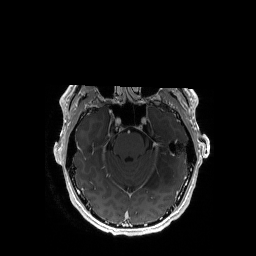
Brain MRI from a brain-tumour surgery series, one axial slice; position 120 of 192 along the scan axis; T1-weighted post-contrast; 1 mm slice thickness; 256 × 256 image matrix, field of view 256 × 256 mm. From the clinical record (not read from this slice): histopathology: Astrocytoma; WHO grade: 3; IDH mutation: yes; tumour location: Left Temporal.
Outlined on this slice (outlined manually by an expert reader):
- tumour: bounding box (x1, y1, x2, y2) in pixels: (147, 117, 177, 189)